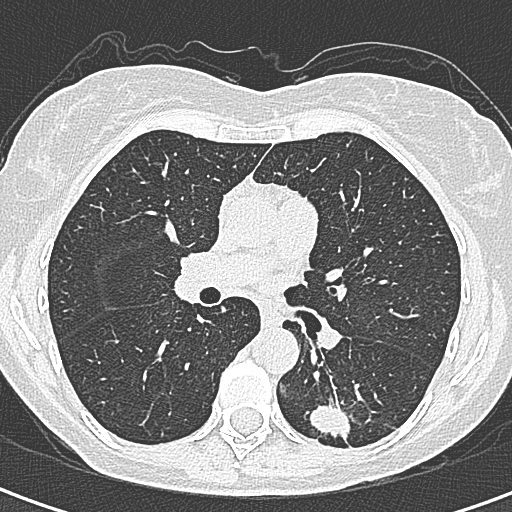
Axial slice from a low-dose chest CT screening exam; baseline screening round; lung window (W 1500 / L -600 HU); 1 mm slice thickness; slice 137 of 328 in the series. Female, age 58 years at enrolment. Former smoker at enrolment.
• Expert reader's lesion annotation, box from (x=297, y=386) to (x=366, y=456) px.
• The screening reader recorded 2 non-calcified nodules or masses ≥4 mm on this exam (left lower lobe, right lower lobe); which of them this box marks is not recorded.
• Later outcome: lung cancer diagnosed 22 days after this screen — adenocarcinoma, NOS, left lower lobe, moderately differentiated (G2), stage IA (AJCC 6th edition), 25 mm at pathology.